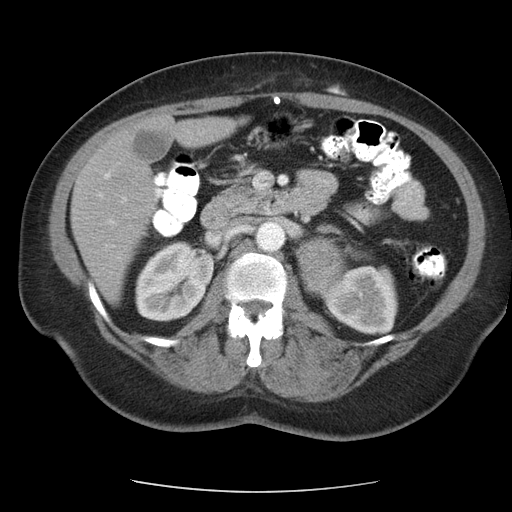
Contrast-enhanced abdominal CT, one axial slice; position 61 of 95 along the scan axis; 120 kVp; soft-tissue window (W 400 / L 40 HU); 512 × 512 image matrix. Patient: female, 71 years. Case-level facts recorded for this patient, not image findings: diagnosis: adrenocortical carcinoma; tumour side: left adrenal; tumour size at pathology: 8.8 cm; Ki-67 index: 20 %; stage (as recorded): 2.
Outlined on this slice (semi-automatically segmented with operator editing):
- mass: bounding box [x1, y1, x2, y2] px = [300, 237, 342, 292]